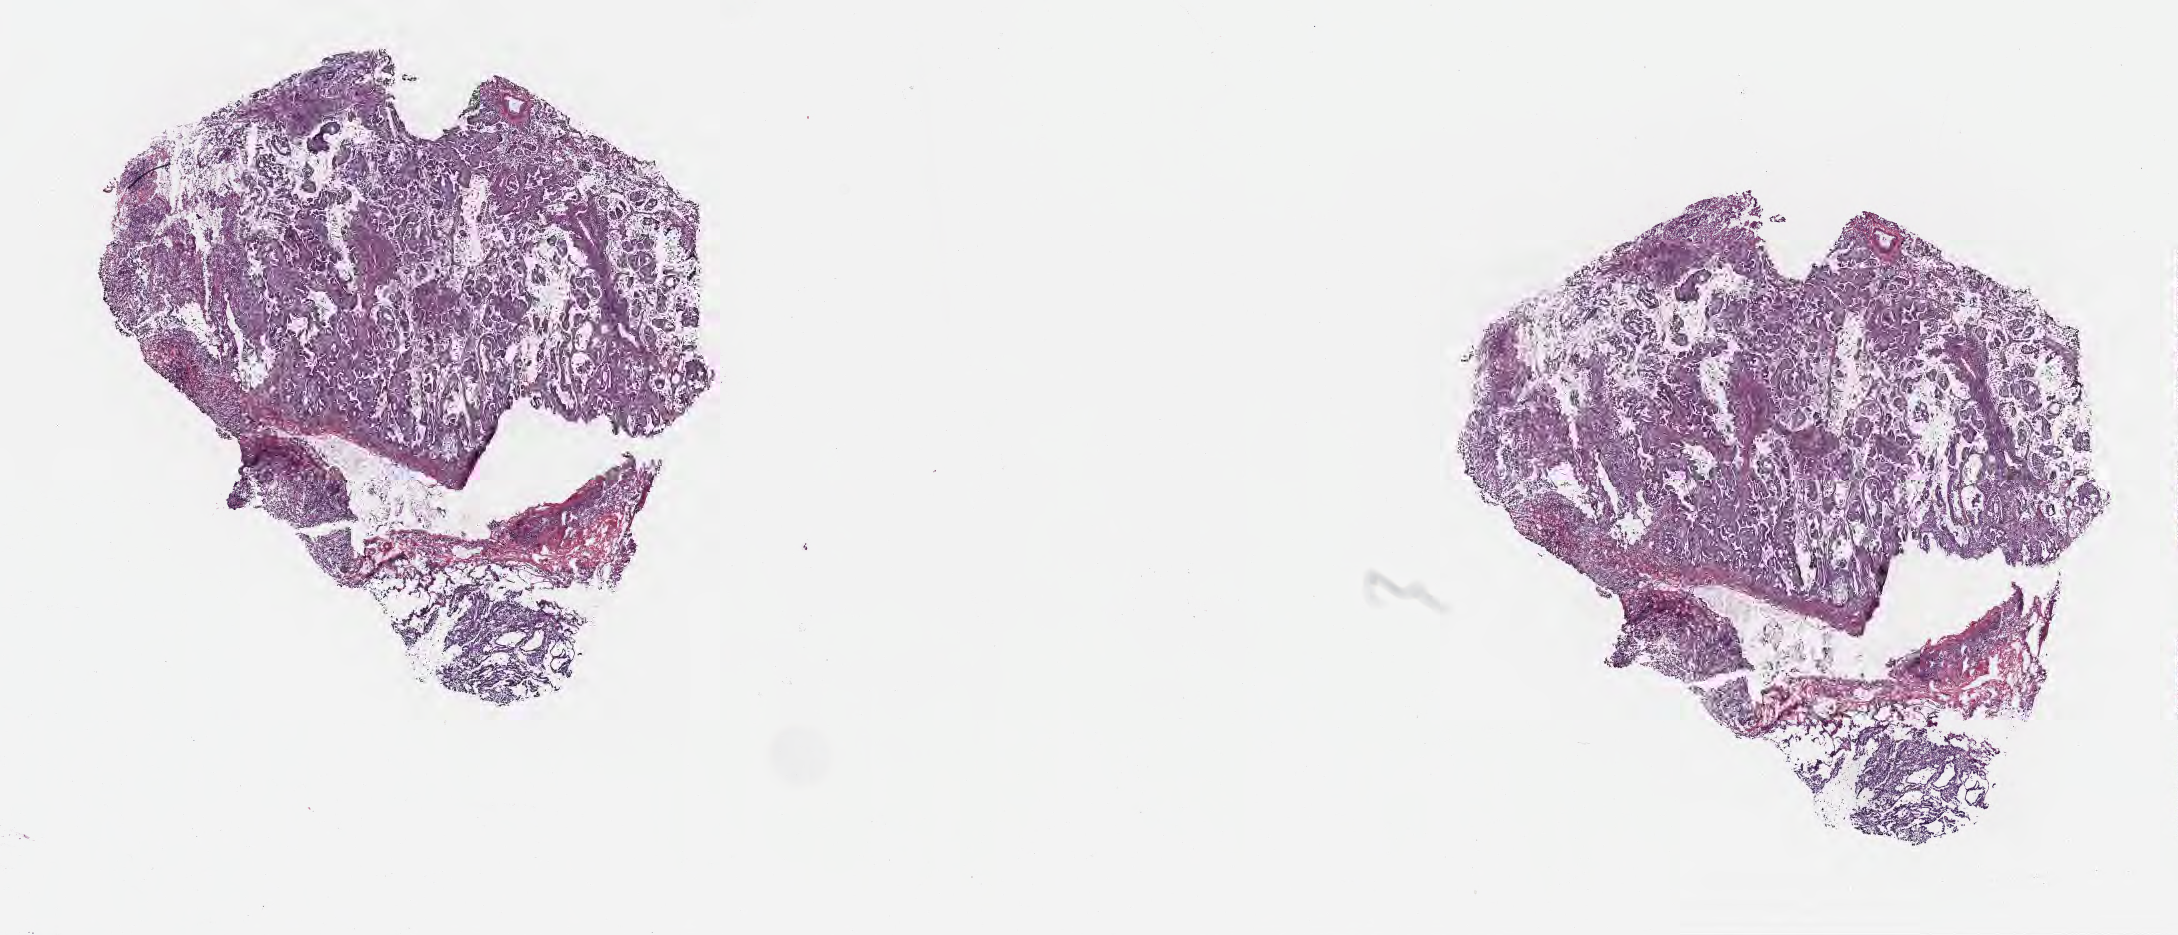
Whole-slide image, hematoxylin and eosin (H&E) stain, a low-resolution overview of the entire scanned area, about 17.6 x 7.6 mm; cryosection; specimen: primary tumor; site: lower lobe of right lung. Patient female; aged 50. Slide review estimates, as recorded: tumor cells 50%, tumor nuclei 60%, stromal cells 45%, necrosis 0%, normal cells 5%. Inflammatory infiltration, as recorded: lymphocyte infiltration 60%, monocyte infiltration 40%, neutrophil infiltration 0%.
Histologic diagnosis: Adenocarcinoma with mixed subtypes. AJCC pathologic stage: Stage IIIA.